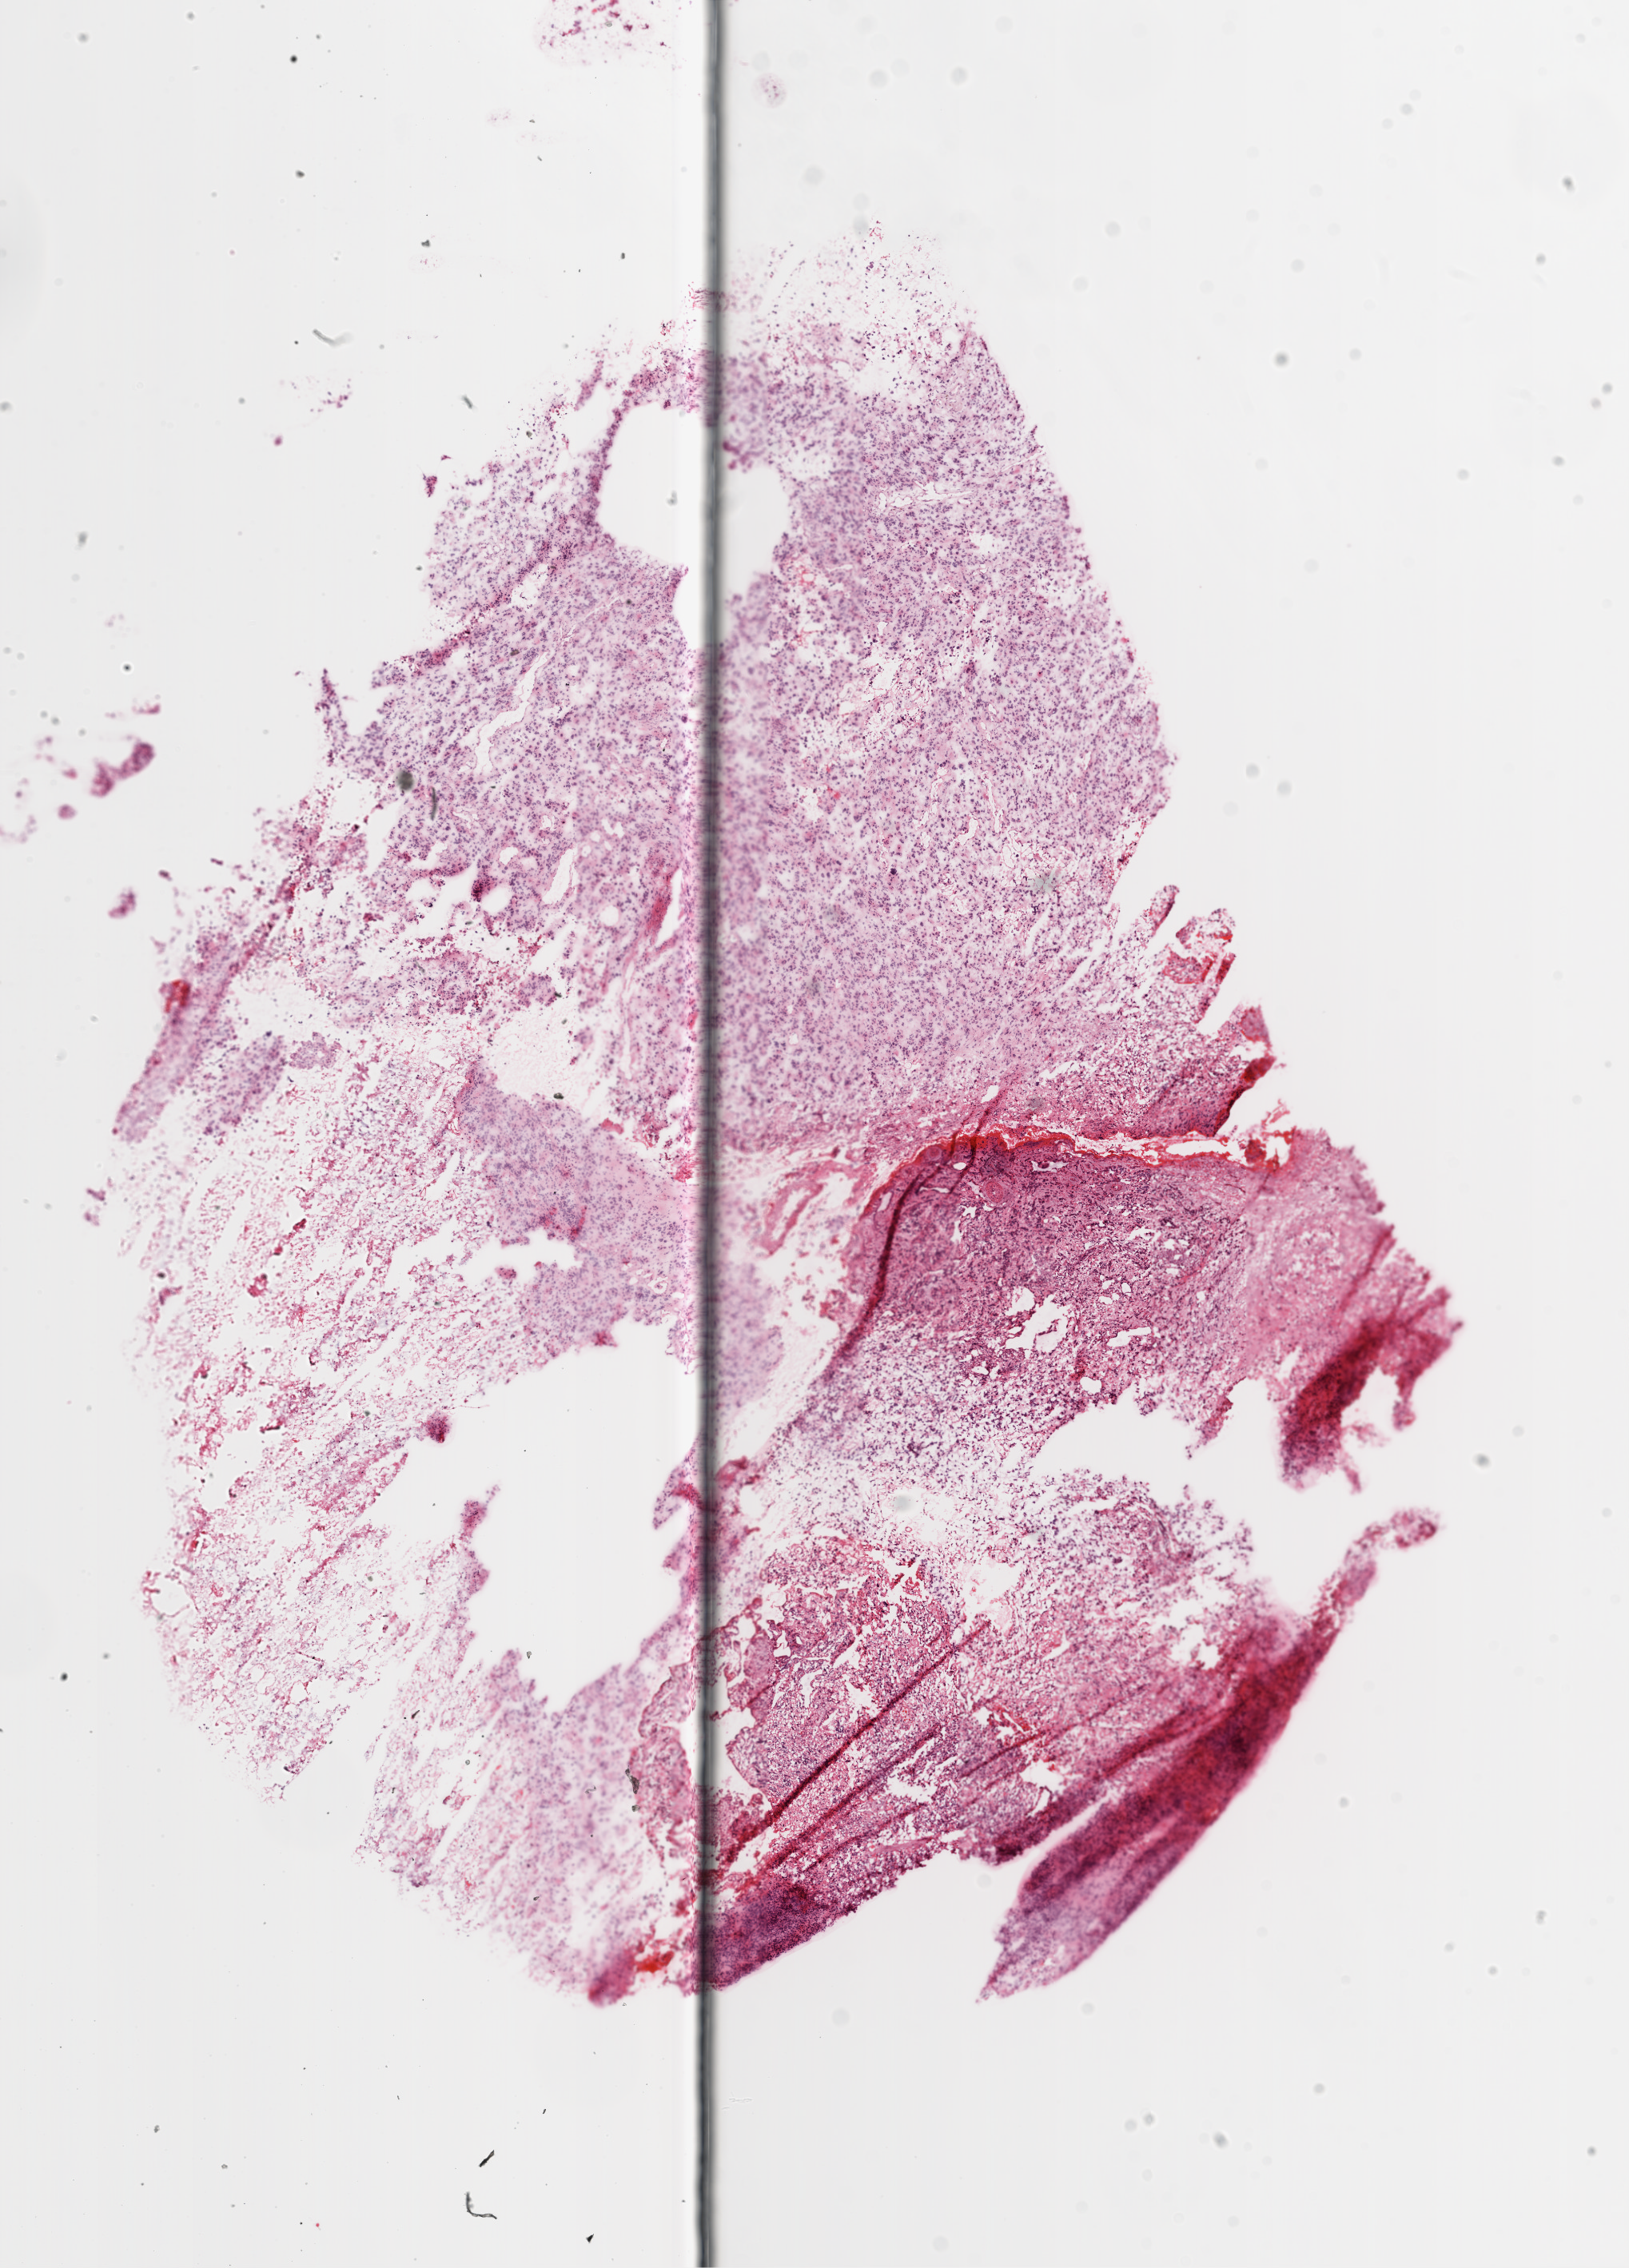
Digitized H&E tissue section (whole slide) — whole scanned area (about 8.2 x 11.4 mm, slide scanned at 20x) shown as a low-resolution overview, frozen section from the bottom of the tissue portion, brain, primary tumour sample. Patient: male, age at initial diagnosis 58 years. Pathologist review of this section (percent, as recorded): tumour cells 60%, tumour nuclei 85%, normal cells 0%, stromal cells 5%, necrosis 35%.
Histologic diagnosis: Glioblastoma.